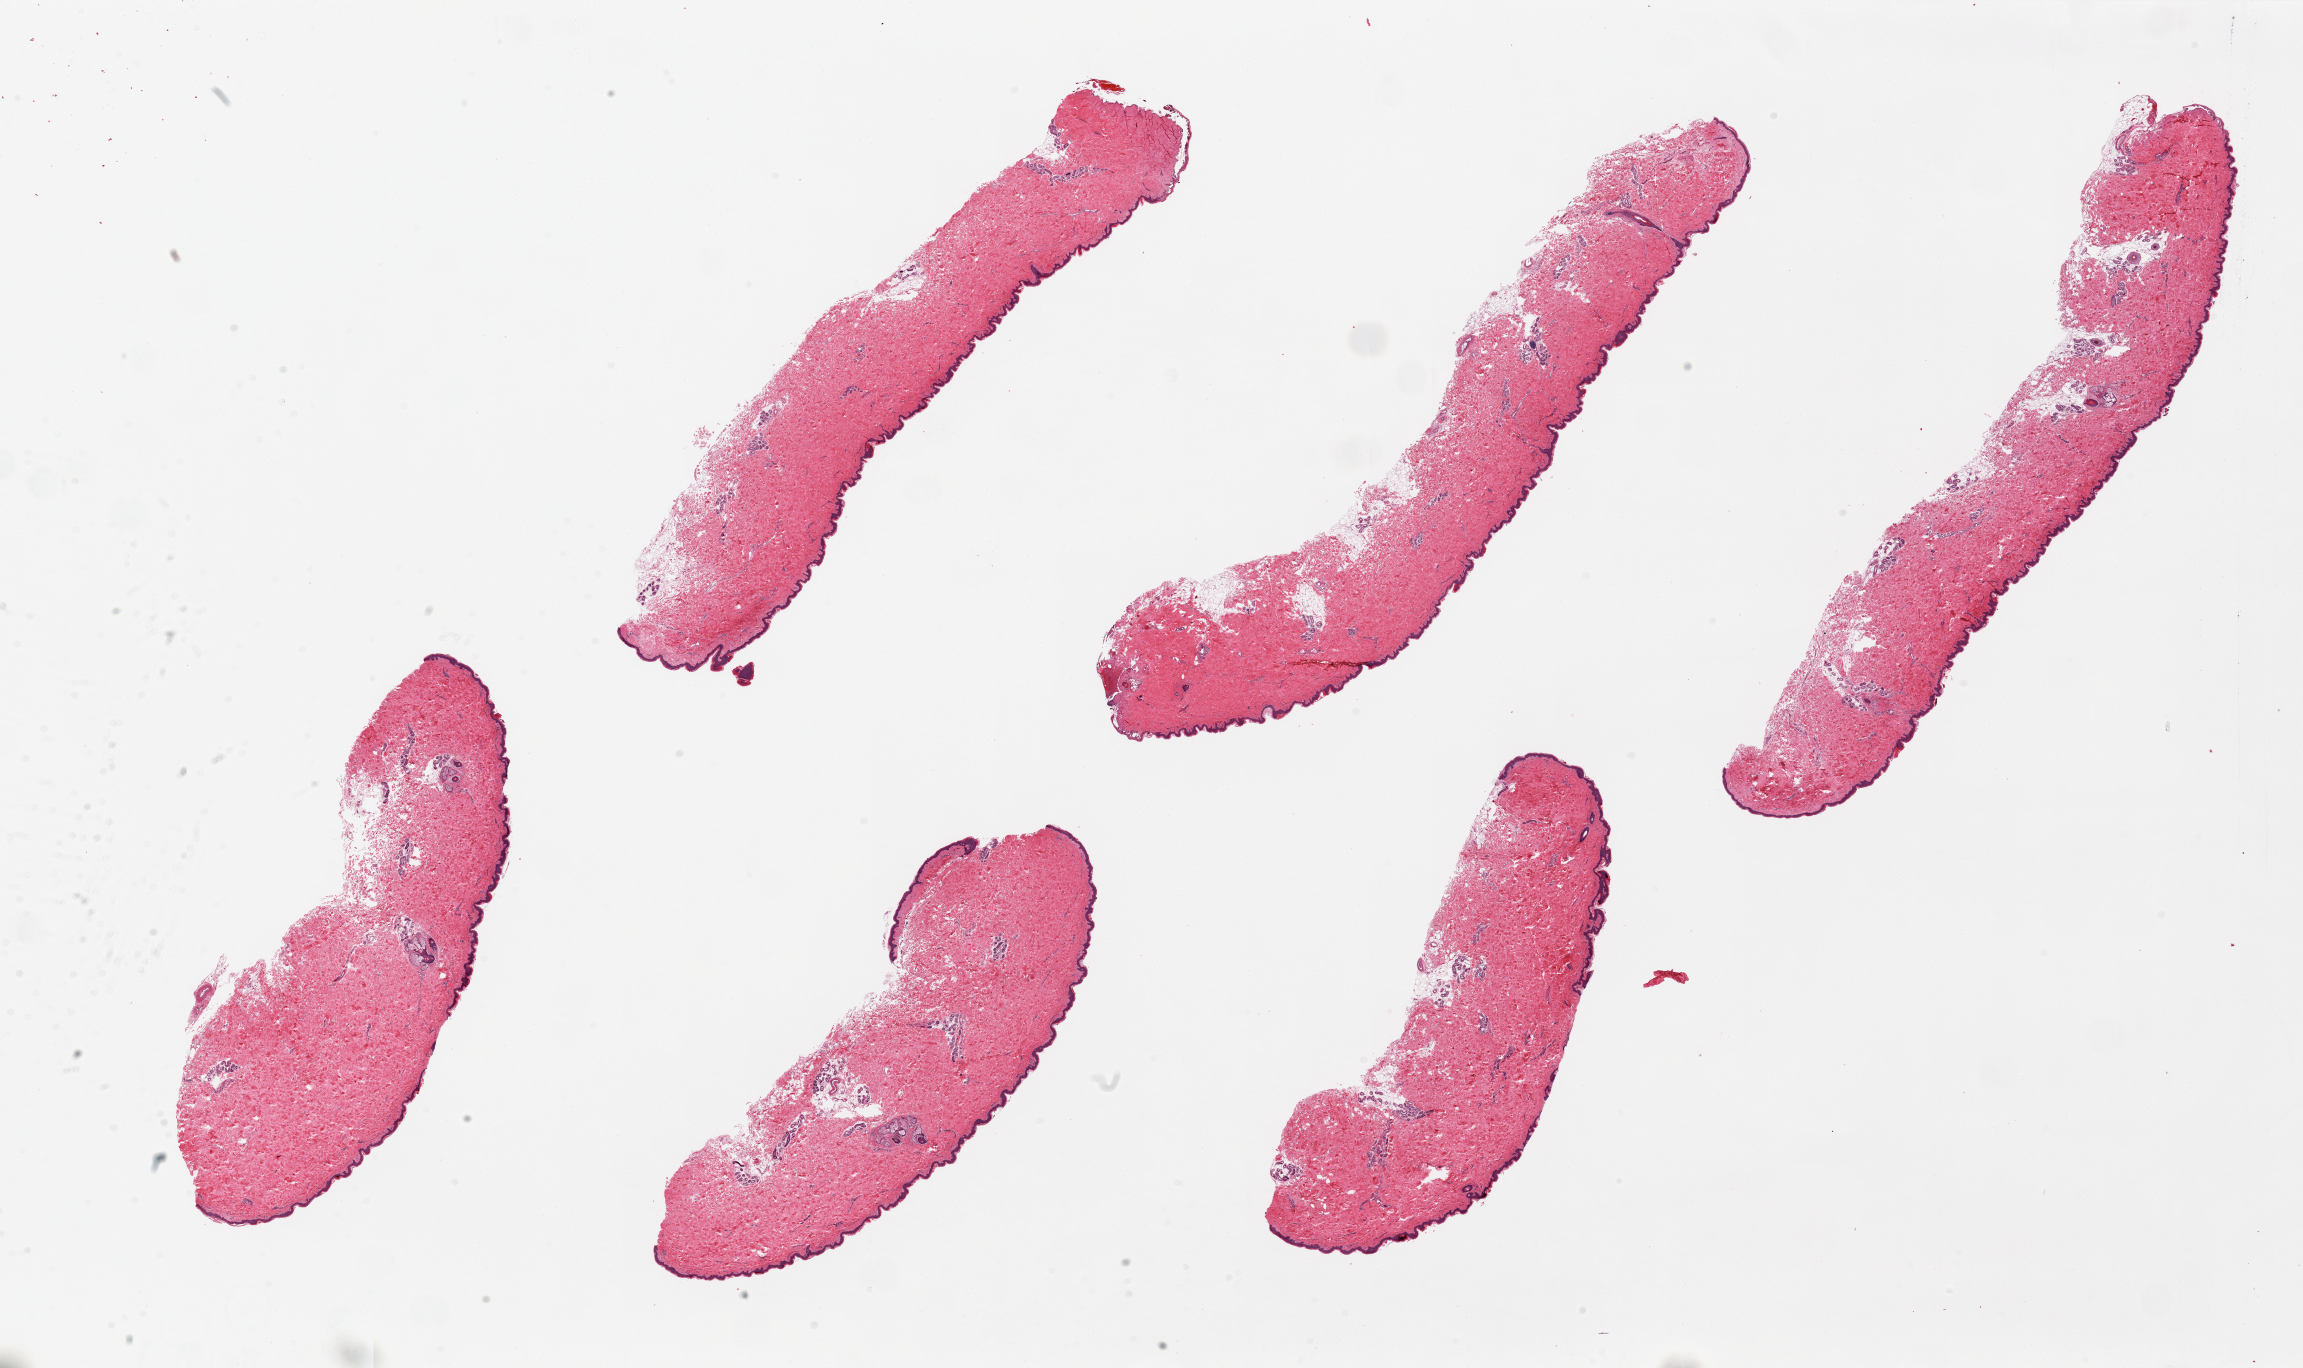
Digitized haematoxylin and eosin-stained section, whole scanned area (about 36.4 x 21.6 mm, from a 20x scan) shown as a low-resolution overview, PAXgene-fixed, paraffin-embedded tissue, target tissue: skin of suprapubic region, donor tissue sample. Female donor.
Pathologist's review note for this sample: 6 pieces. up to 14x3mm; Well dissected, largely free of subcutaneous adipose.